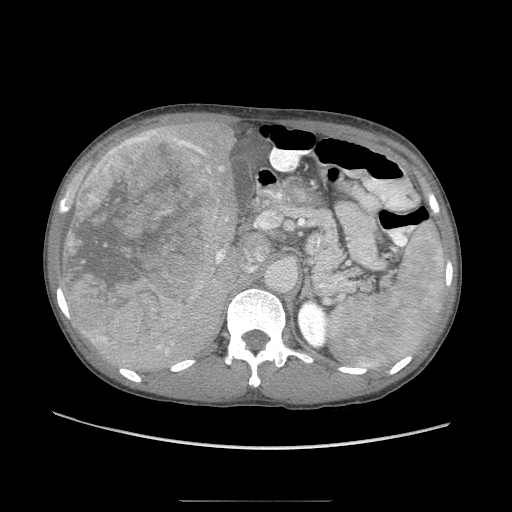
Contrast-enhanced abdominal CT (liver protocol), one axial slice. Position 51 of 103 along the scan axis. Reconstruction kernel STANDARD. 120 kVp. Soft-tissue window (W 400 / L 40 HU). 2.5 mm slice thickness. 512 × 512 image matrix, field of view 380 × 380 mm. Case-level facts recorded for this patient, not image findings: diagnosis: hepatocellular carcinoma (patient treated with transarterial chemoembolisation; whether this scan precedes or follows treatment is not stated here); TNM stage (as recorded): Stage-IIIA; Child-Pugh class: A.
Annotated regions visible in this slice (semi-automatically segmented with operator editing):
- liver parenchyma outside the tumour (the mass and vessels are separate outlines, so this box may not span the whole liver): bounding box (x1, y1, x2, y2) in pixels: (70, 116, 254, 382)
- mass: (61, 128, 219, 345)
- liver vessels: (120, 149, 216, 372)